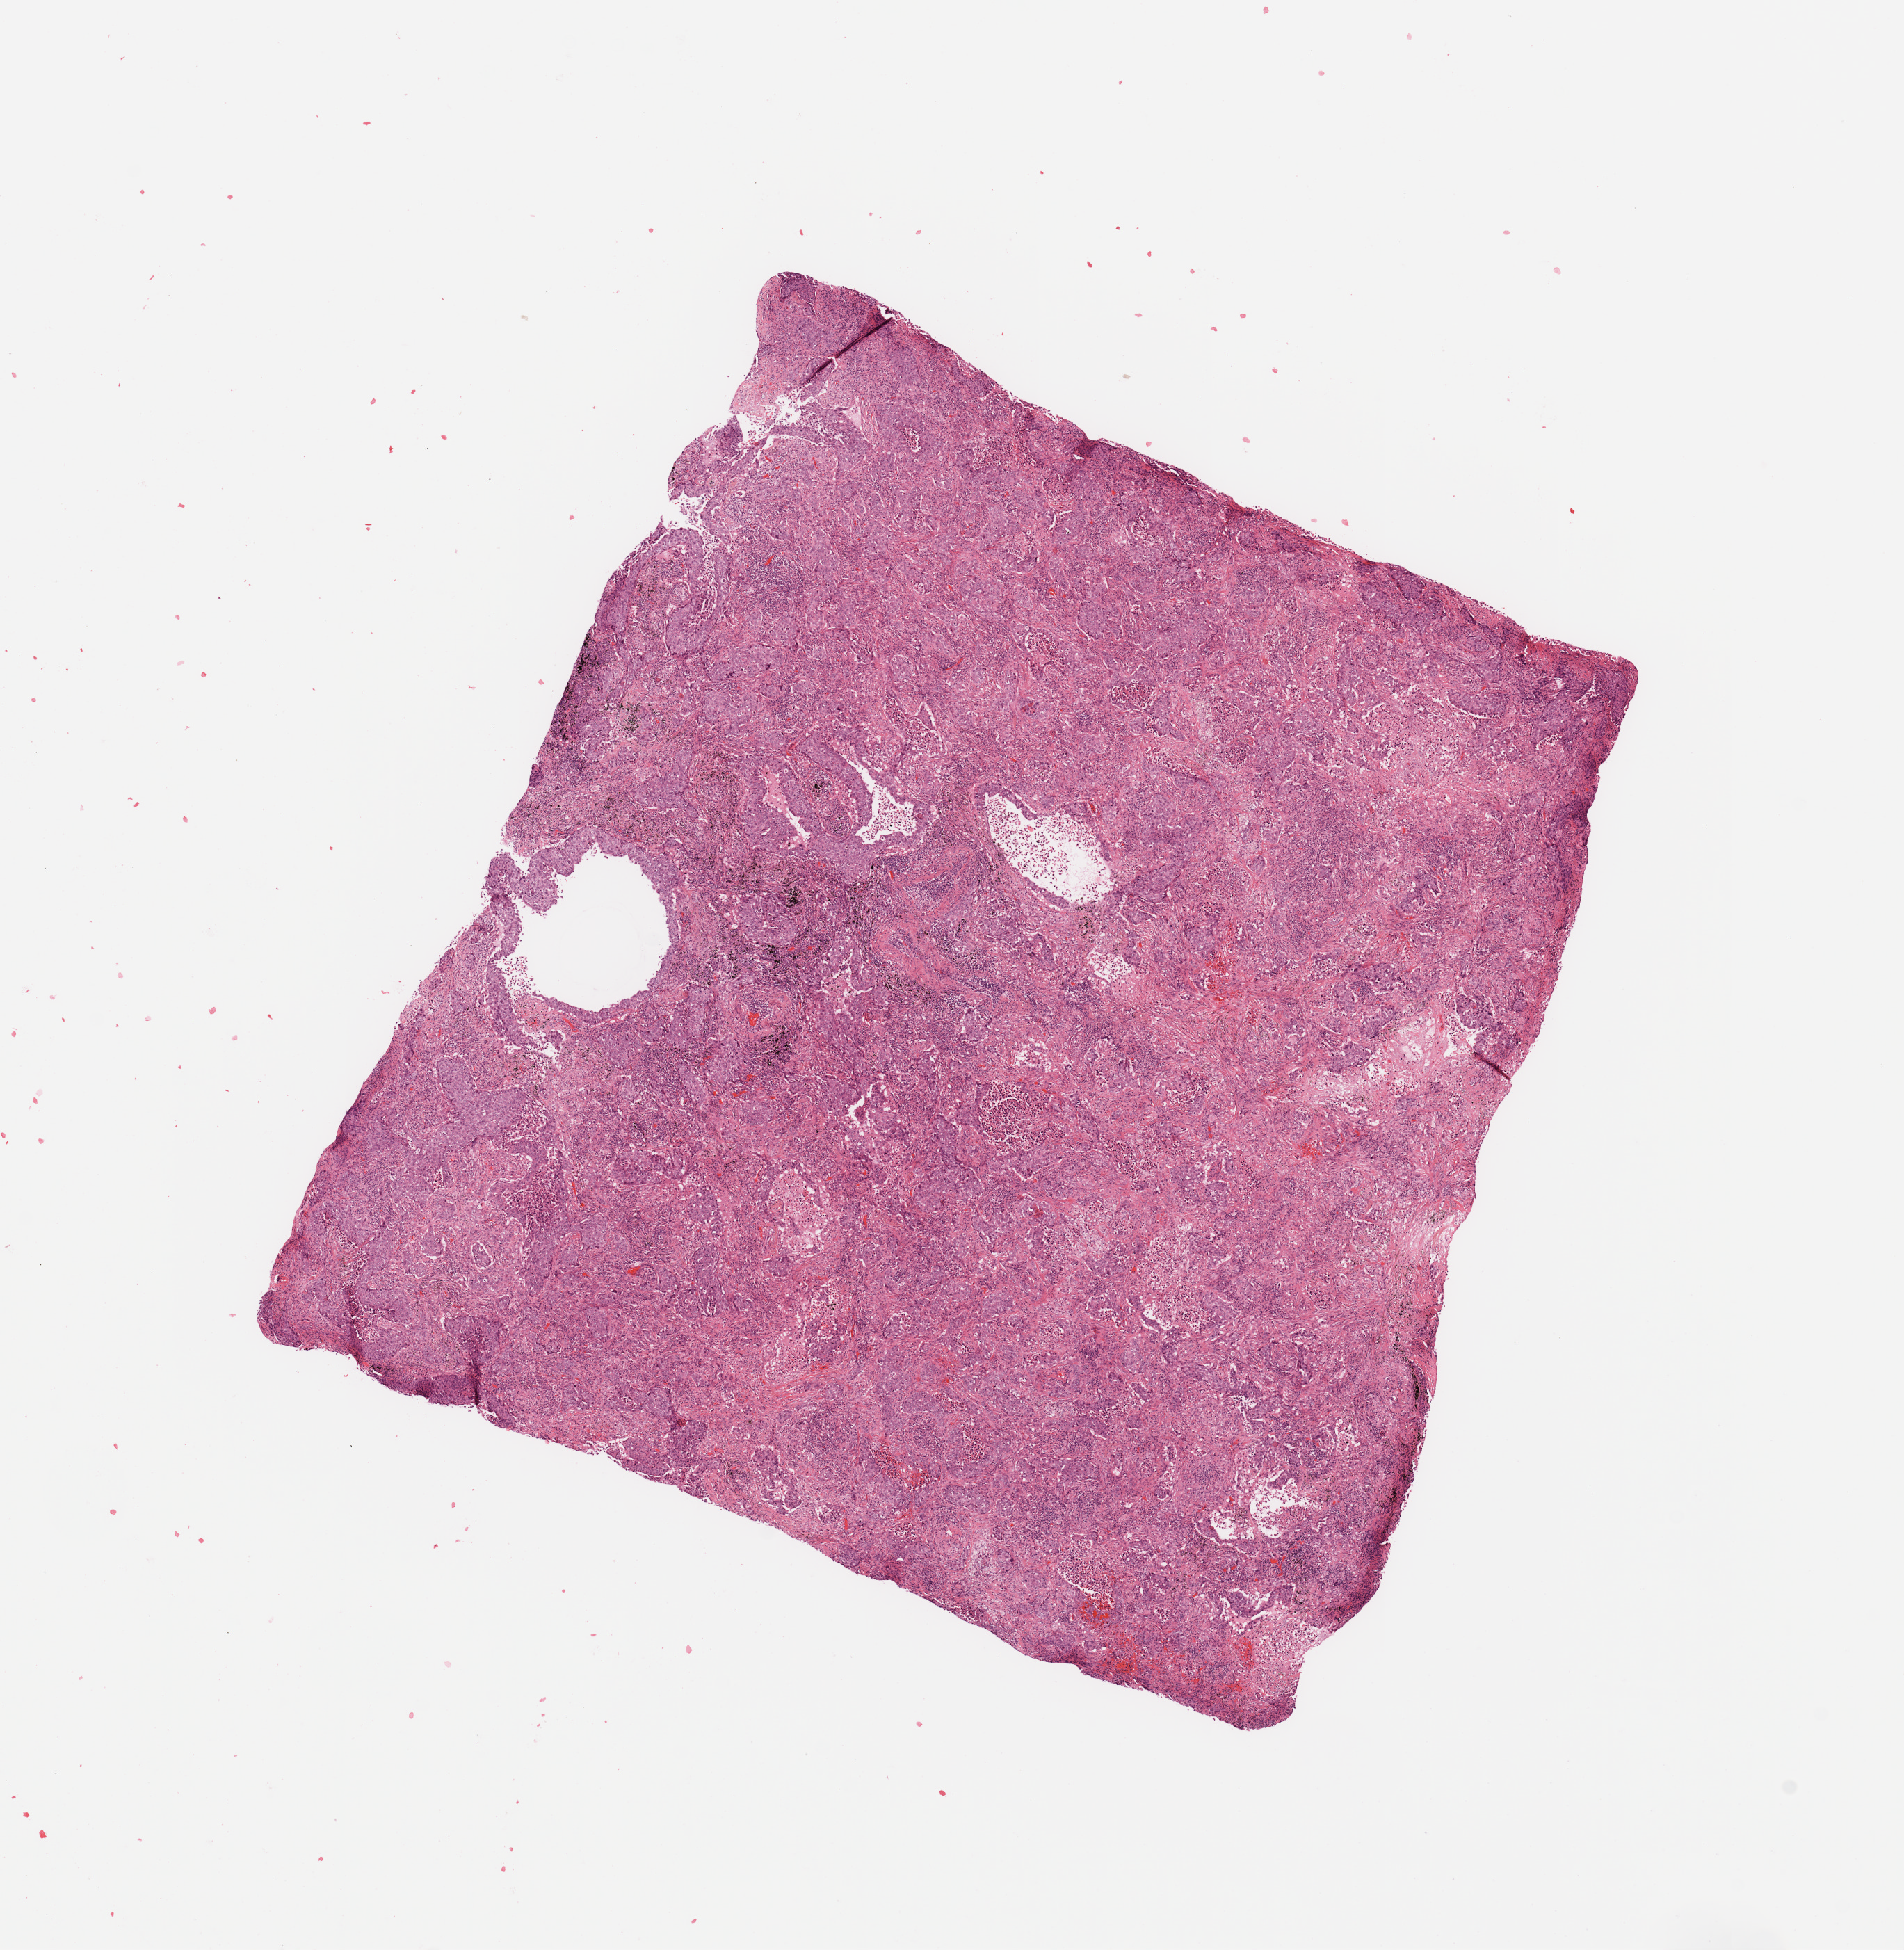
Whole-slide histology image, H&E, whole scanned area (about 10.8 x 11.1 mm) shown as a low-resolution overview, lung, tumour tissue. 72-year-old male patient. Histologic grade: G3 (poorly differentiated).
• diagnosis: Adenocarcinoma, NOS
• primary tumour site (as recorded): left lower lobe
• AJCC pathologic stage: IIB